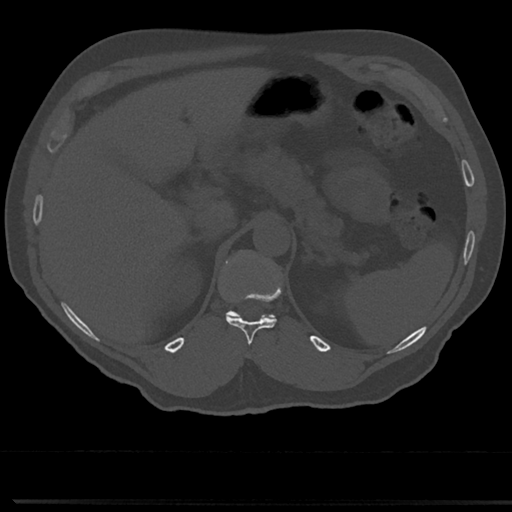
CT including the spine, one axial slice. Slice 183 of 817 in the series (ordered by position). Reconstruction kernel Br40s/3. Bone window (W 1800 / L 400 HU). 0.5 mm slice thickness. 512 × 512 image matrix, field of view 355 × 355 mm. Patient: male, 61 years. From the clinical record (not read from this slice): primary cancer: prostate.
Annotated regions visible in this slice (semi-automatic segmentation, software-assisted and operator-edited):
- T11 vertebra: bounding box <226,293,277,346> (left, top, right, bottom; pixels)
- T12 vertebra: <224,250,276,320>